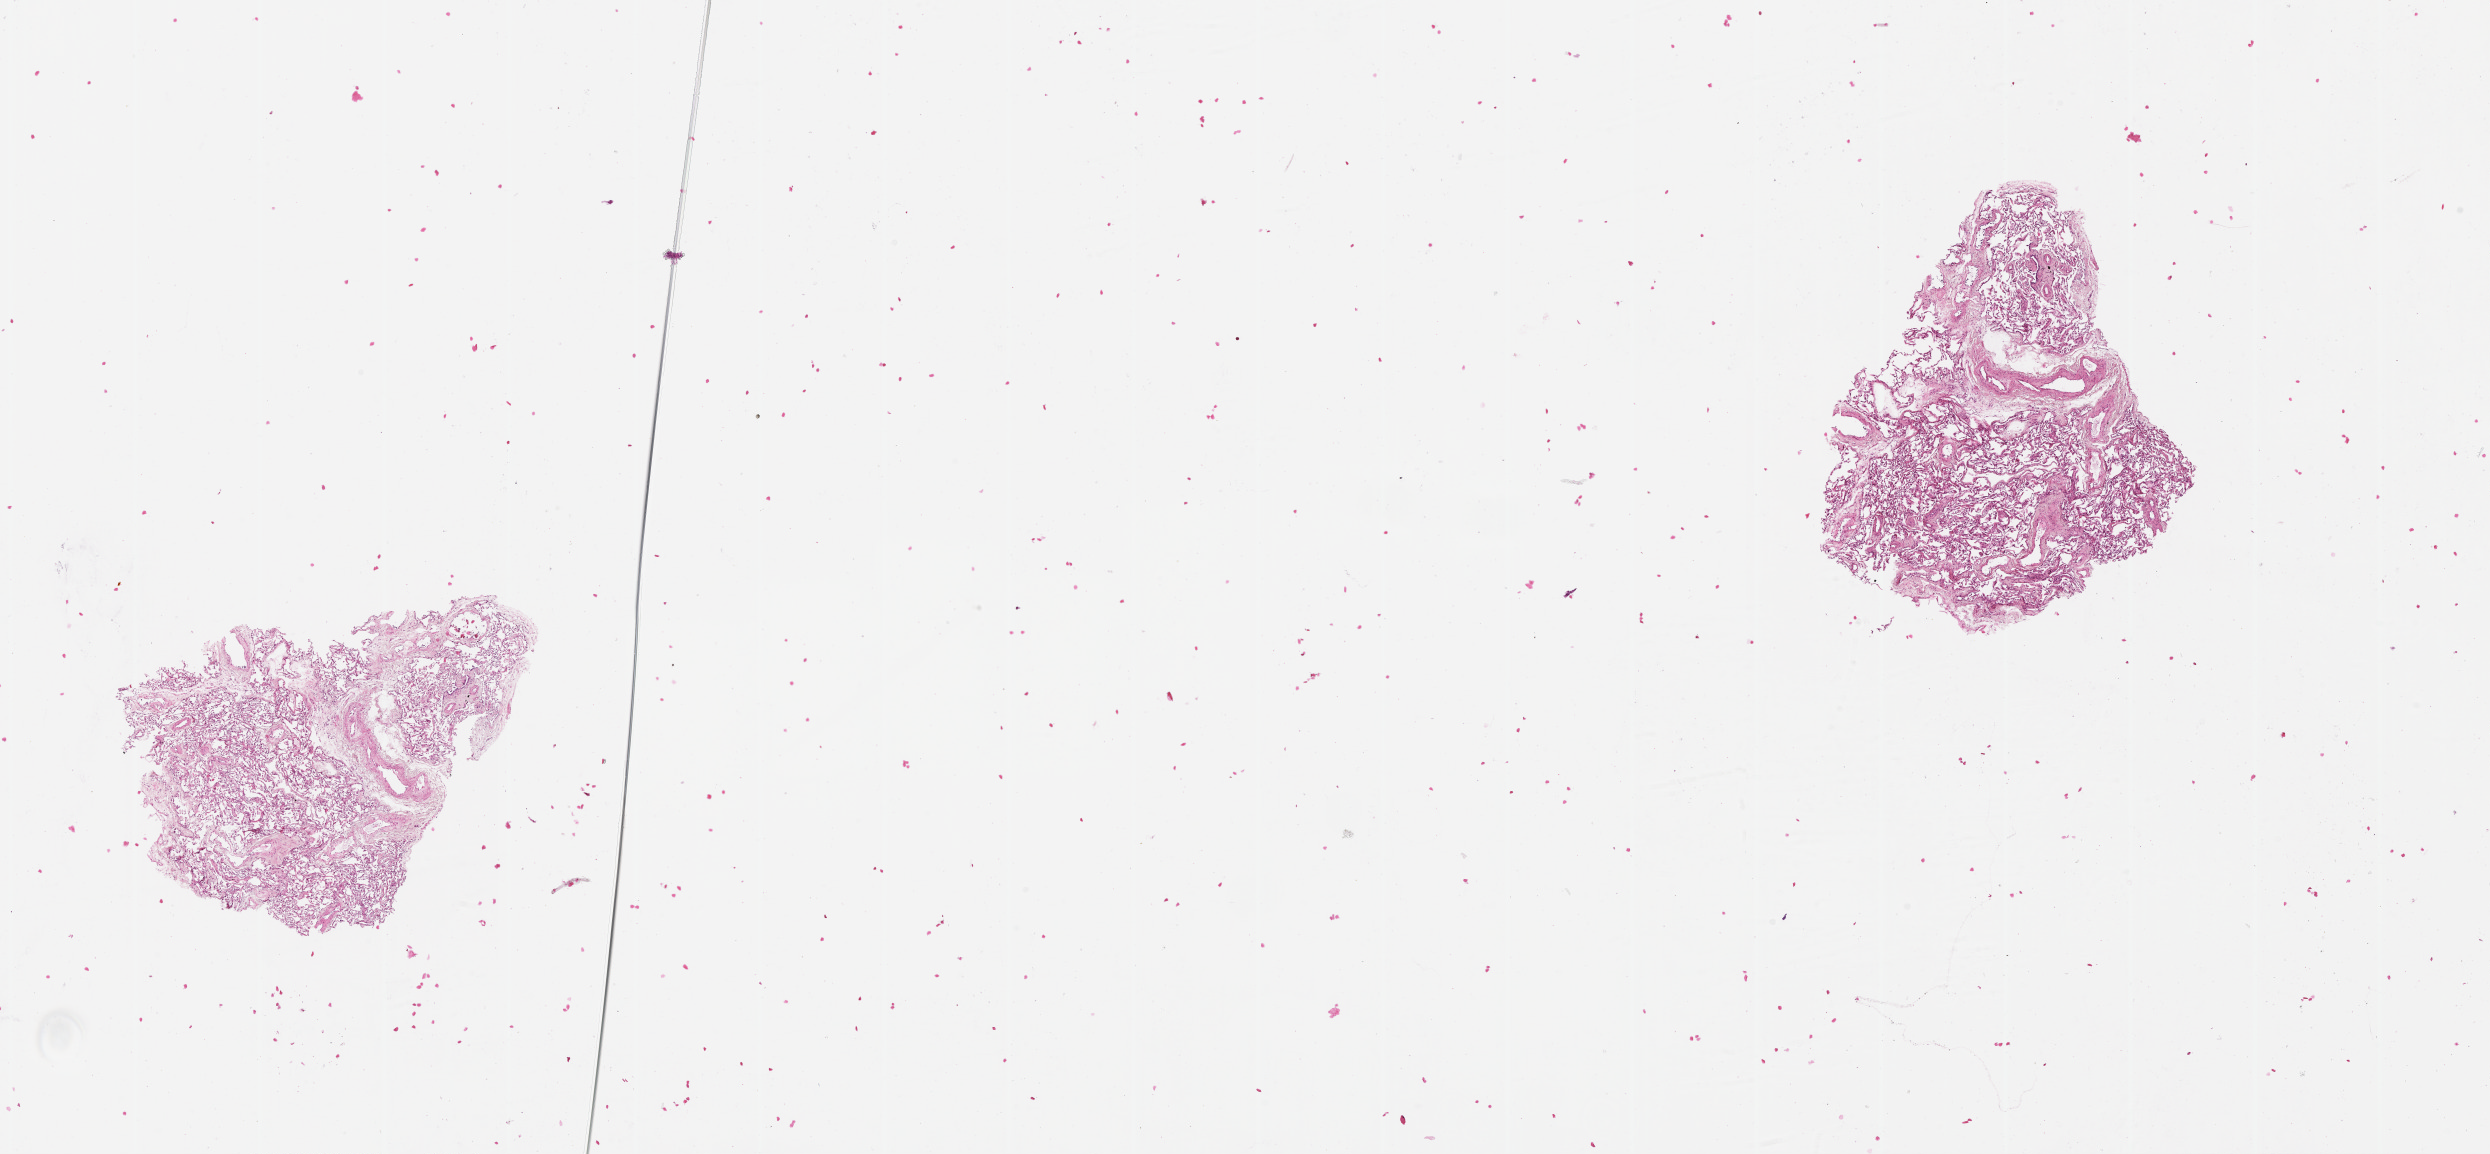
H&E whole-slide image — shown as a low-resolution overview of the whole scanned area (about 20.0 x 9.3 mm). Normal (non-tumour) tissue sample, lung. Male, 60 y/o.
This section: normal (non-tumour) tissue from the same patient. Patient diagnosis (cohort enrolment): squamous cell carcinoma (lung).